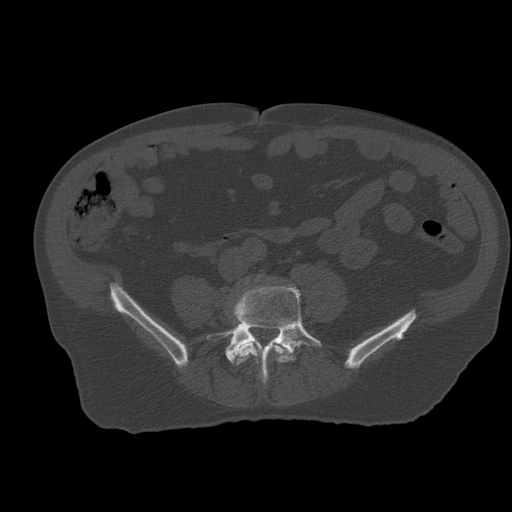
CT including the spine, one axial slice; position 149 of 399 along the scan axis; 120 kVp; bone window (W 1800 / L 400 HU); 1.25 mm slice thickness; 512 × 512 image matrix. Patient age 73 years. Case-level facts recorded for this patient, not image findings: primary cancer: prostate; vertebrae with lytic lesions (as recorded): L2.
Structures marked on this image (semi-automatically segmented with operator editing):
- L4 vertebra: bounding box <235,342,290,385> (left, top, right, bottom; pixels)
- L5 vertebra: <208,287,322,385>